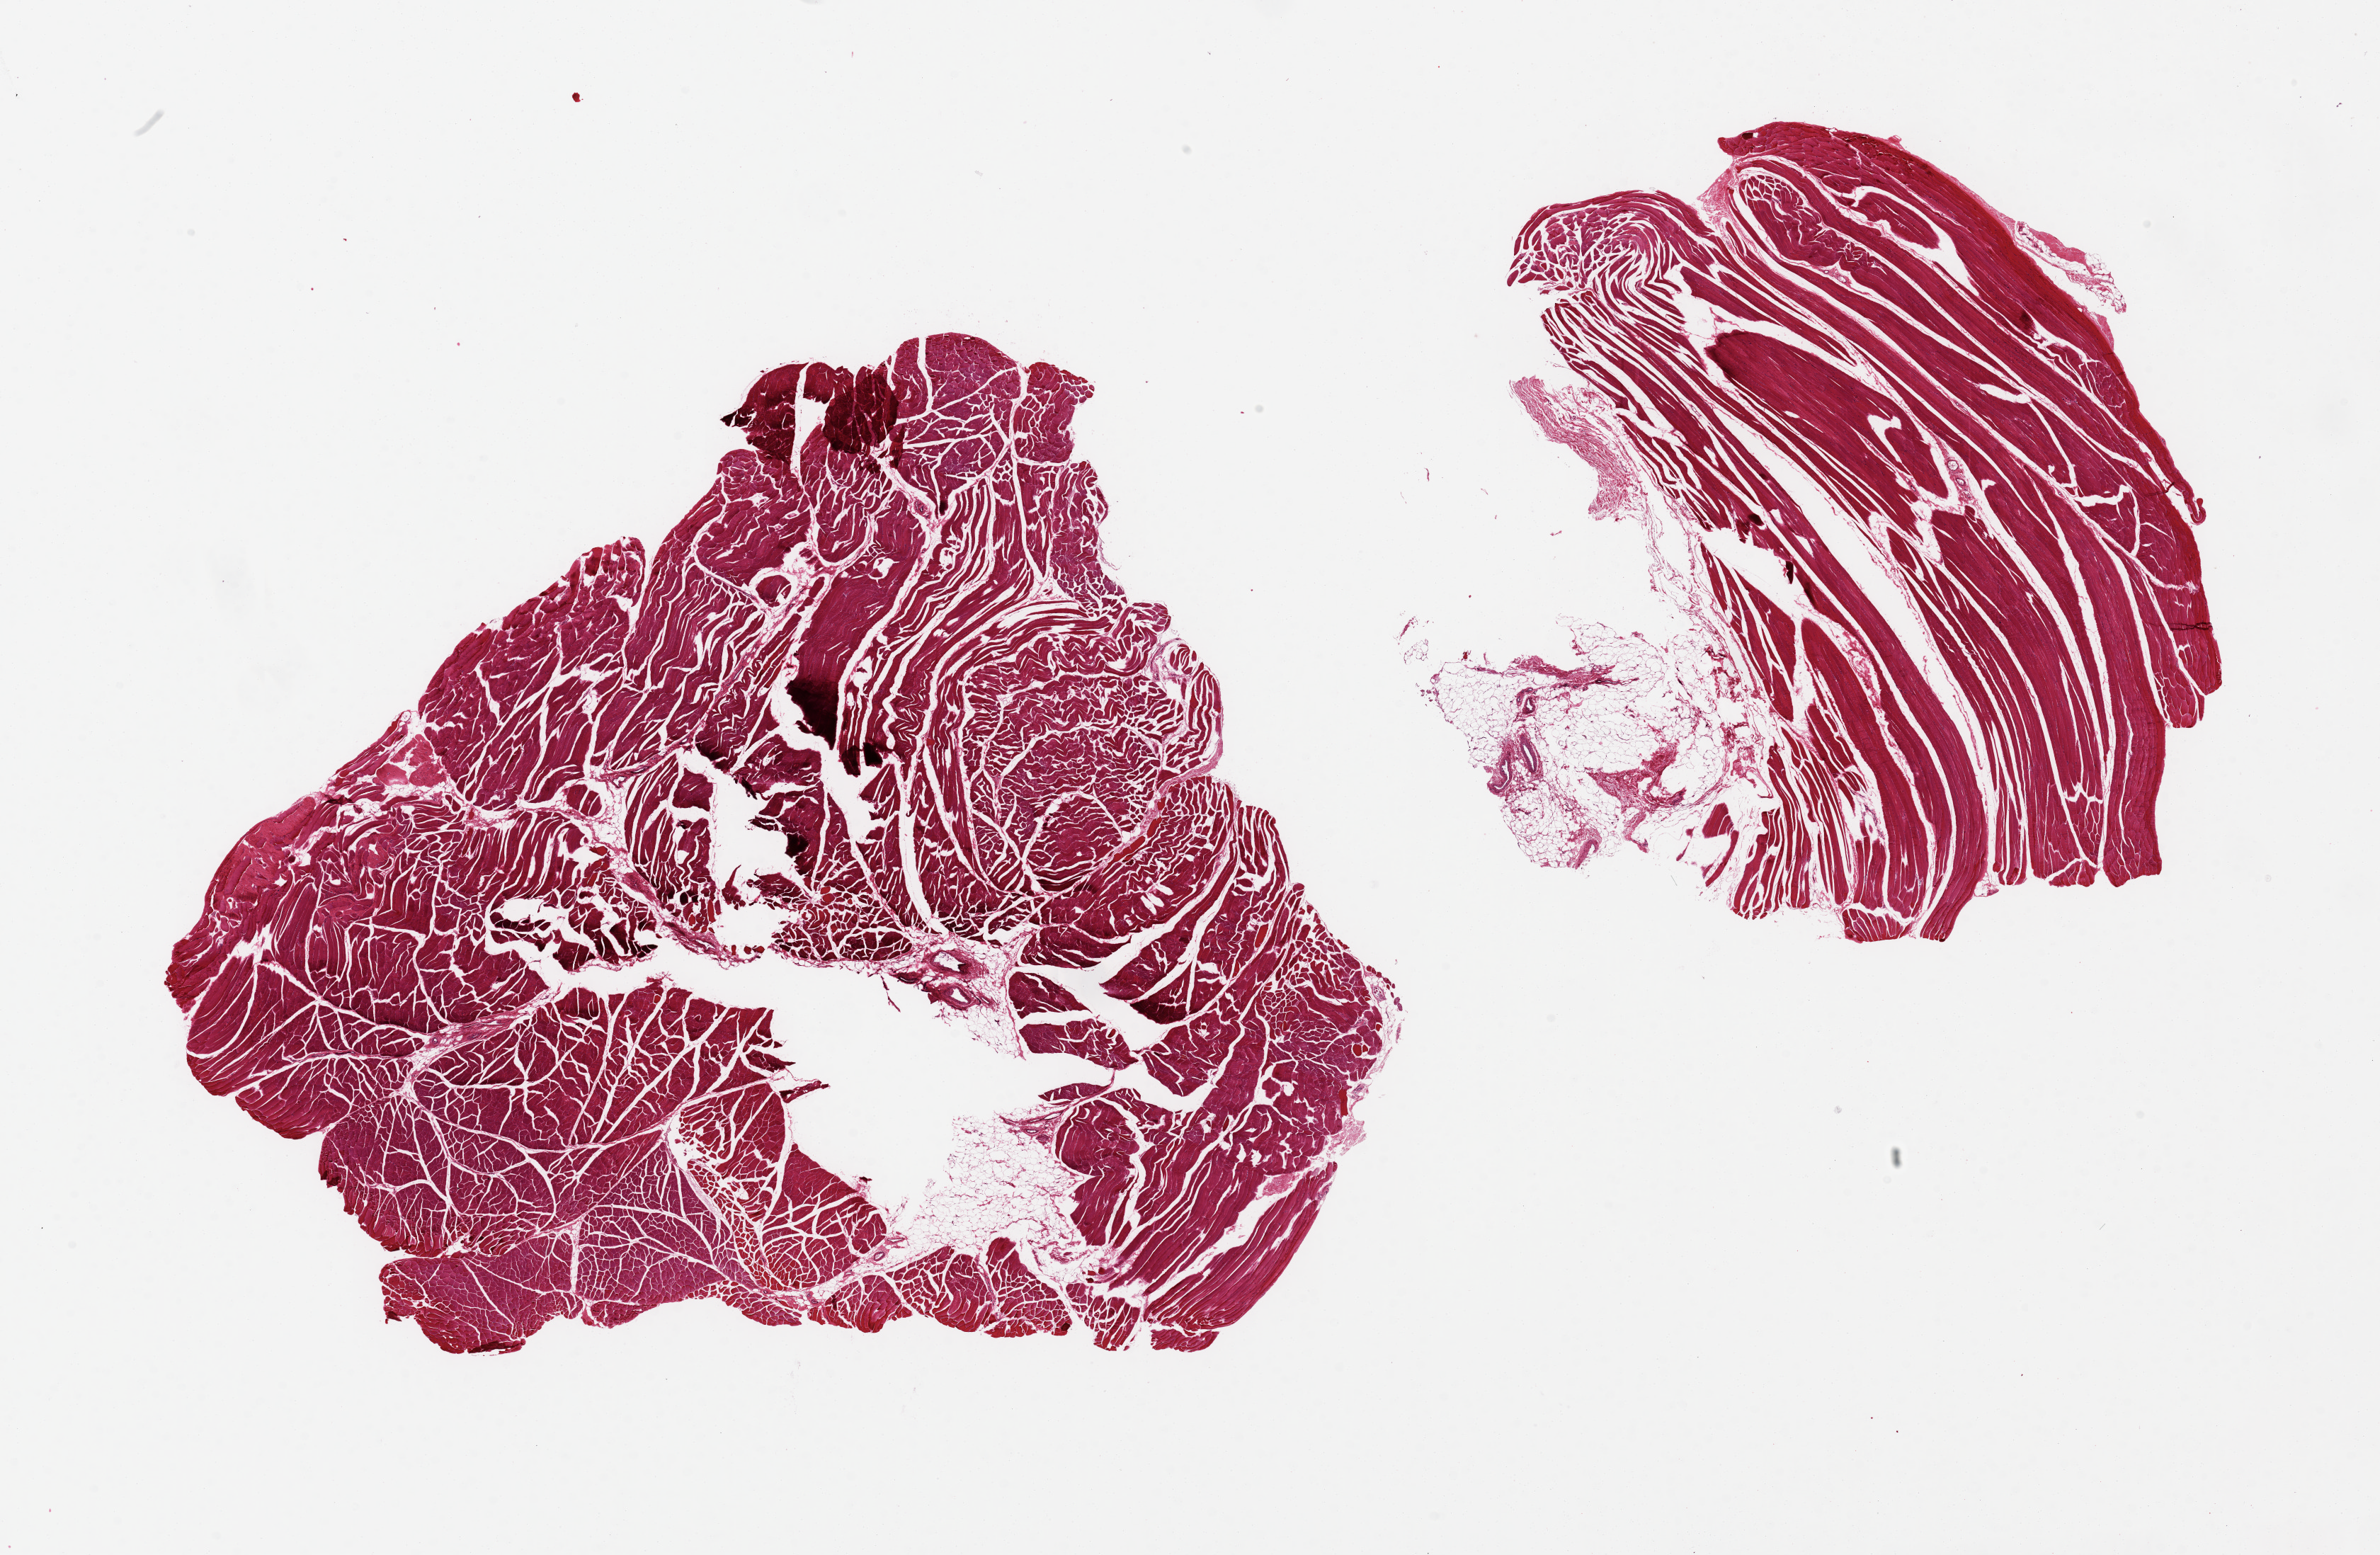
Whole-slide image, H&E stain, brightfield — whole scanned area (about 26.6 x 17.4 mm) shown as a low-resolution overview, PAXgene-fixed paraffin-embedded (PFPE) section, section of skeletal muscle (target tissue), donor tissue sample. Donor: female.
Pathologist's review note for this sample: 2 pieces 12x10 & 10x7 mm; larger piece has numerous tissue artifacts, e.g. fractures; smaller piece has 3x3 mm adipose on one surface.